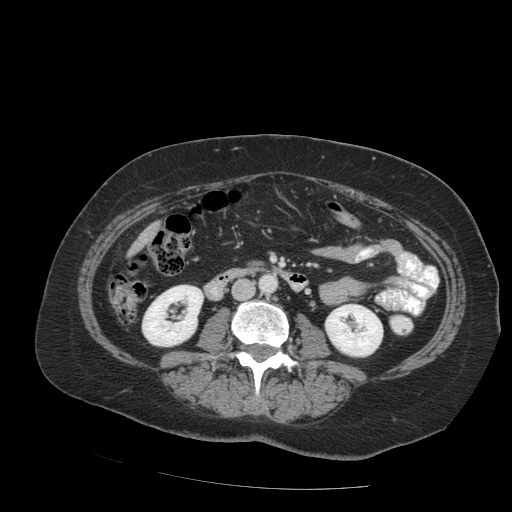
Contrast-enhanced abdominal CT (liver protocol), one axial slice; slice 18 of 99 in the series (ordered by position); reconstruction kernel STANDARD; soft-tissue window (W 400 / L 40 HU); 2.5 mm slice thickness; 512 × 512 image matrix, field of view 400 × 400 mm. From the clinical record (not read from this slice): diagnosis: hepatocellular carcinoma (patient treated with transarterial chemoembolisation; whether this scan precedes or follows treatment is not stated here); TNM stage (as recorded): Stage-IVB; Child-Pugh class: A; tumour nodularity: uninodular.
Outlined on this slice (semi-automatic segmentation, software-assisted and operator-edited):
- liver parenchyma outside the tumour (the mass and vessels are separate outlines, so this box may not span the whole liver): bounding box (x1, y1, x2, y2) in pixels: (134, 223, 158, 248)